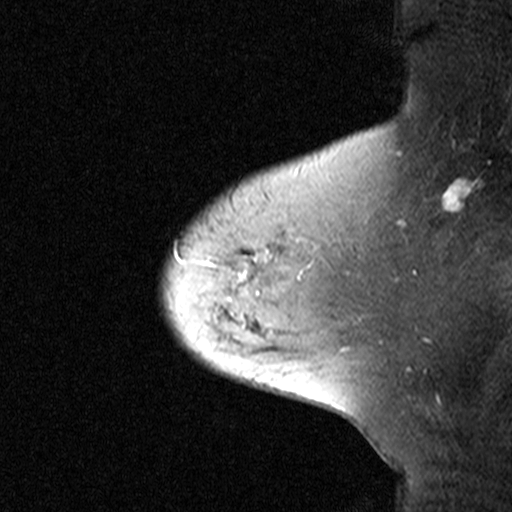
Breast MRI (dynamic contrast-enhanced), one sagittal slice; slice 36 of 44 in the series (ordered by position); dynamic contrast-enhanced study with each time point stored as its own series, time point 2 of 3 at this slice position (early post-contrast, ordered by acquisition time); 1.5 T; TE 4.5 ms, TR 11 ms; 3 mm slice thickness; 512 × 512 image matrix. Female patient, age 65 years. From the clinical record (not read from this slice): setting: breast cancer imaged before/during neoadjuvant chemotherapy; receptor status: HER2-positive.
Annotated regions visible in this slice (semi-automatic segmentation, software-assisted and operator-edited):
- analysis volume of interest (the breast-tissue region the enhancement analysis was run in; not a lesion): bounding box [x1, y1, x2, y2] px = [162, 172, 329, 345]
- tumour enhancement mask (voxels above the 90 % enhancement threshold inside the analysis volume of interest): [241, 256, 269, 280]